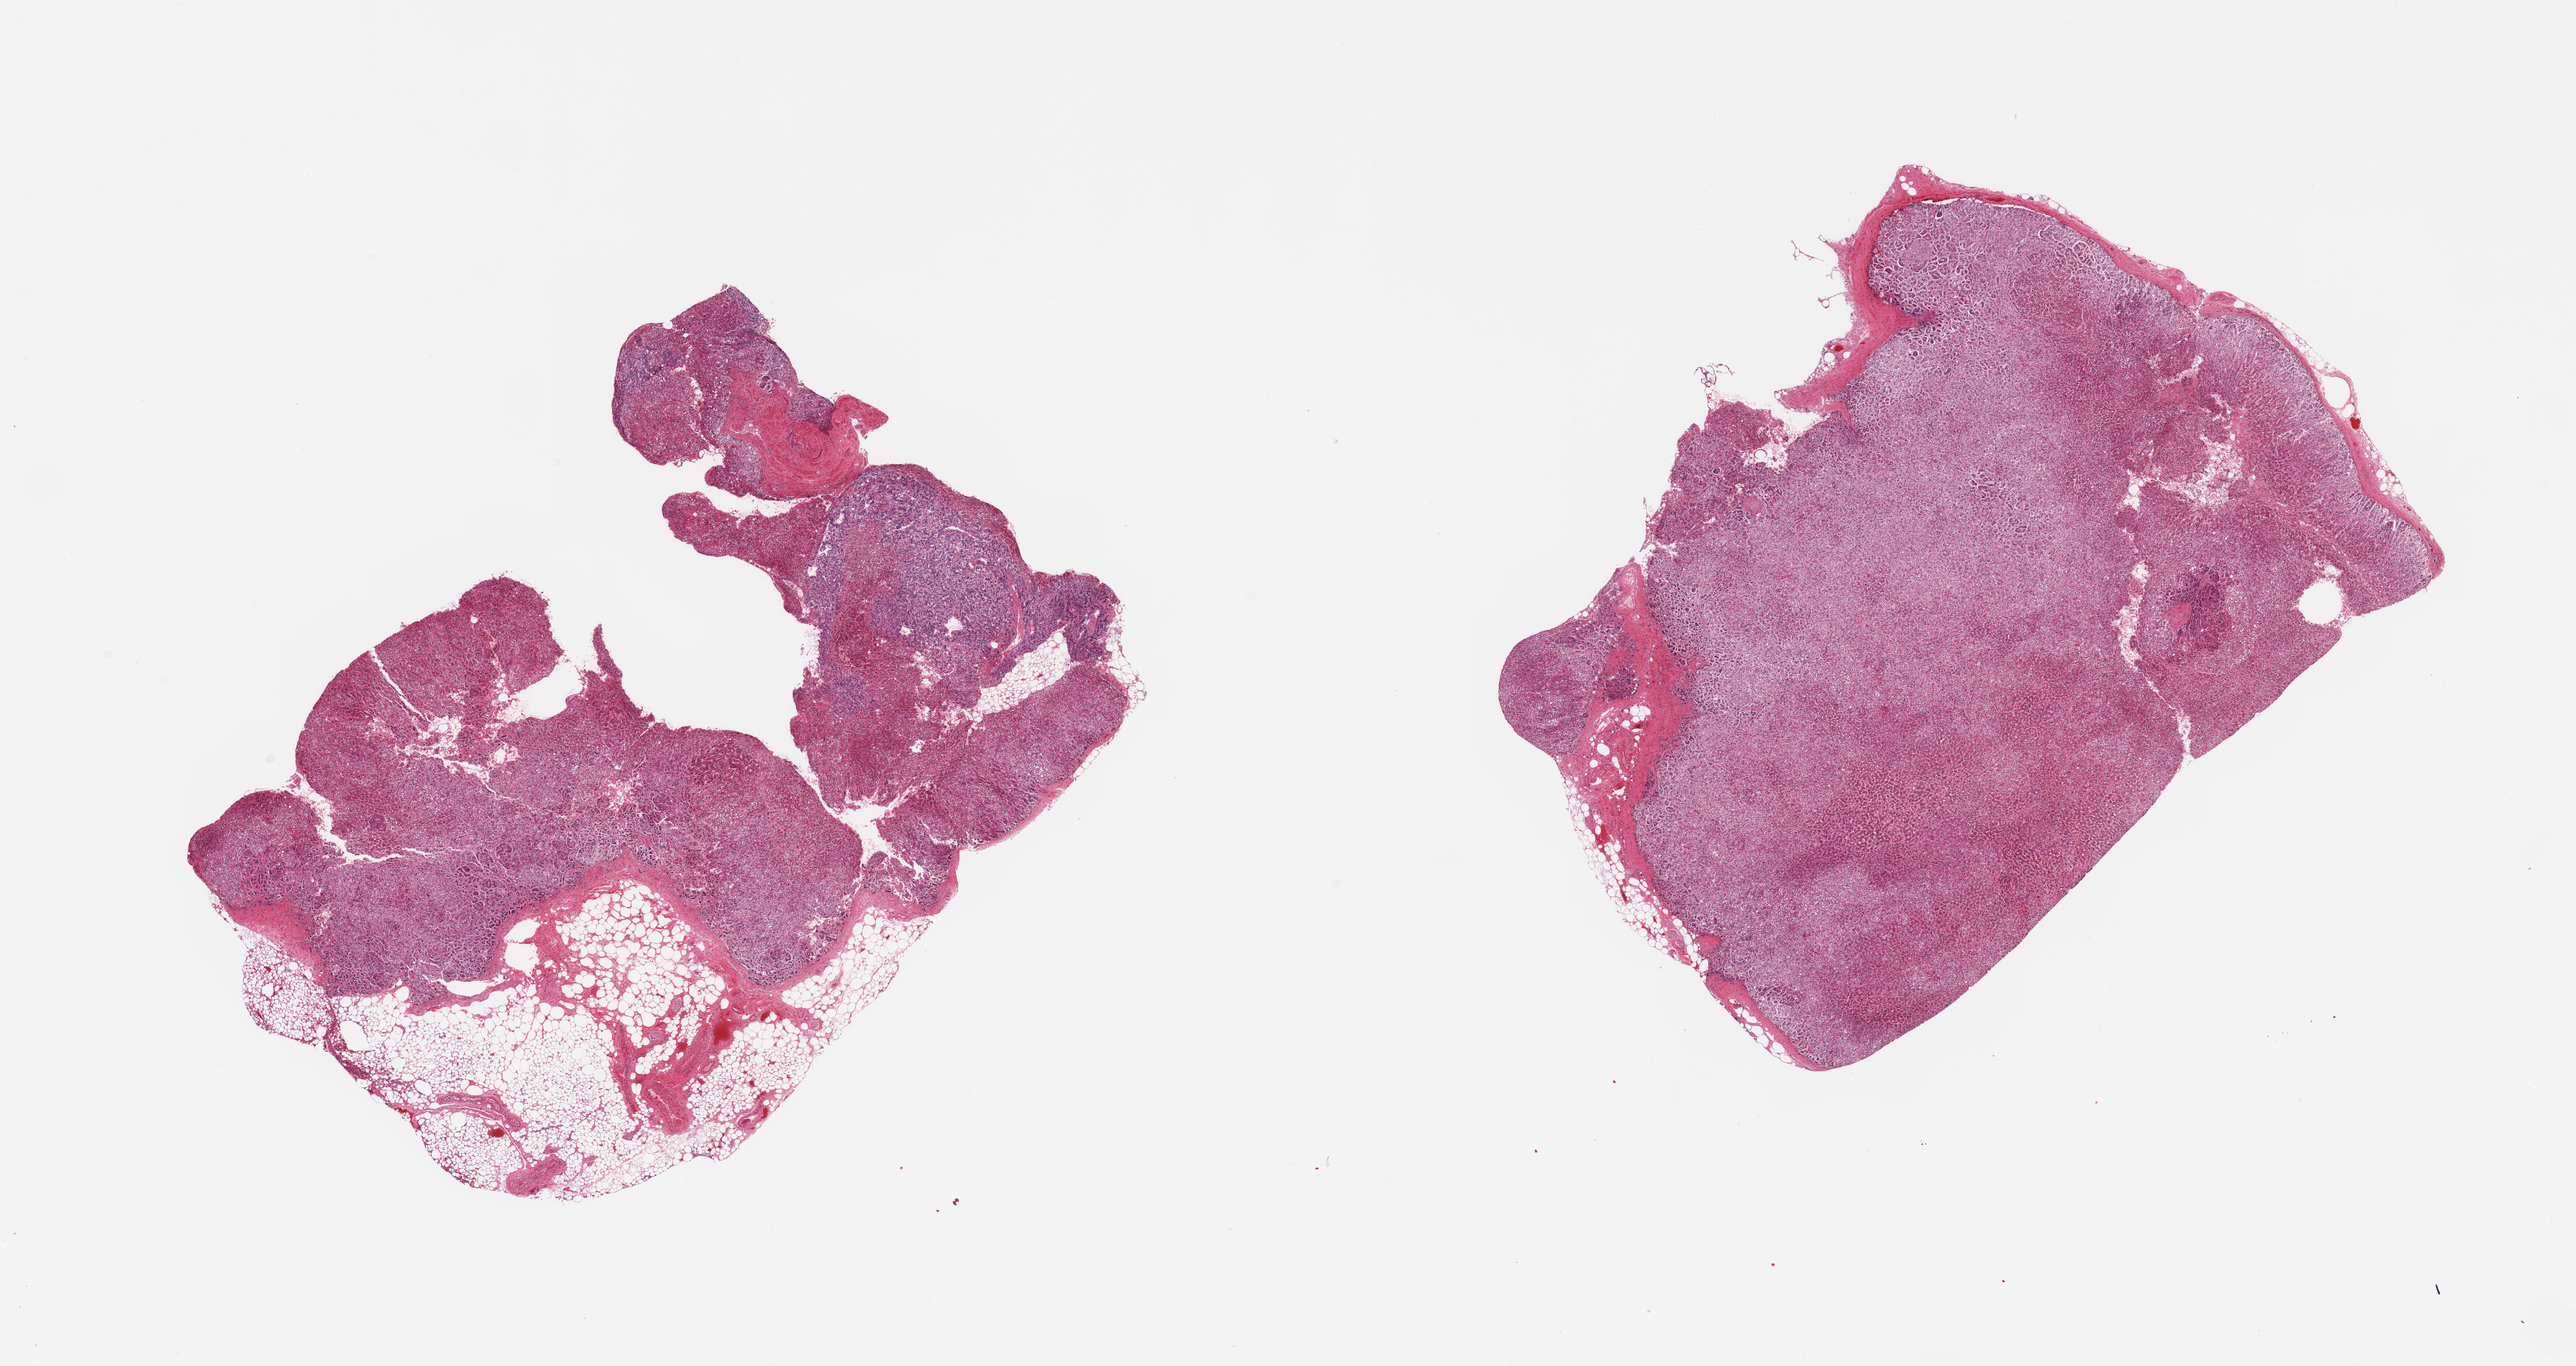
Whole-slide image, haematoxylin and eosin stain, low-resolution overview of the scanned area, about 27.6 x 14.6 mm (slide scanned at 20x). PAXgene-fixed paraffin-embedded (PFPE) section. Section of adrenal gland (target tissue). Tissue donor sample. Donor sex: male.
Pathologist's review note for this sample: 2 pieces; 1 is ~30% fat, adrenal cortex and medulla.